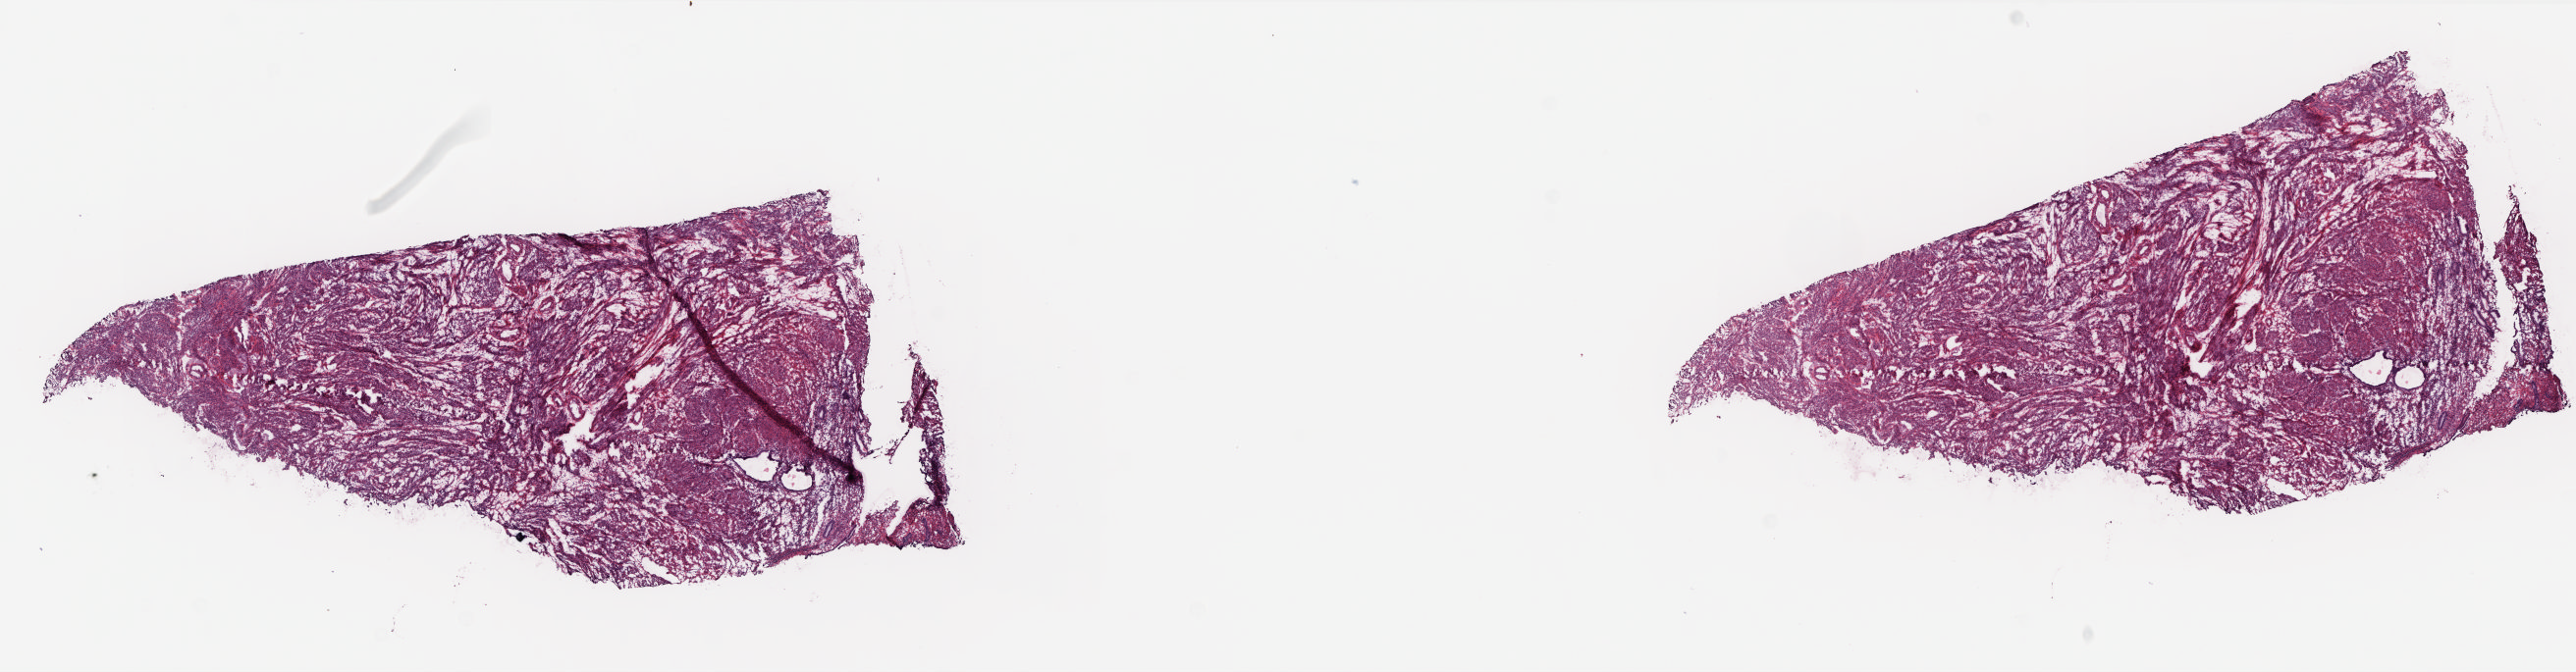
Whole-slide histology image, H&E, low-resolution overview of the scanned area, about 21.0 x 5.5 mm (acquisition: 20x scan); frozen section; sample: solid tissue normal (non-tumour tissue), uterus. Patient: female, age at initial diagnosis 62 years. Pathologist review of this section (percent, as recorded): tumour cells 0%, tumour nuclei 0%, normal cells 100%, stromal cells 0%, necrosis 0%. Inflammatory infiltration, as recorded: lymphocyte infiltration 0%, monocyte infiltration 0%, neutrophil infiltration 0%.
This section: solid tissue normal (non-tumour) sample from the same patient. Patient diagnosis: Leiomyosarcoma, NOS.